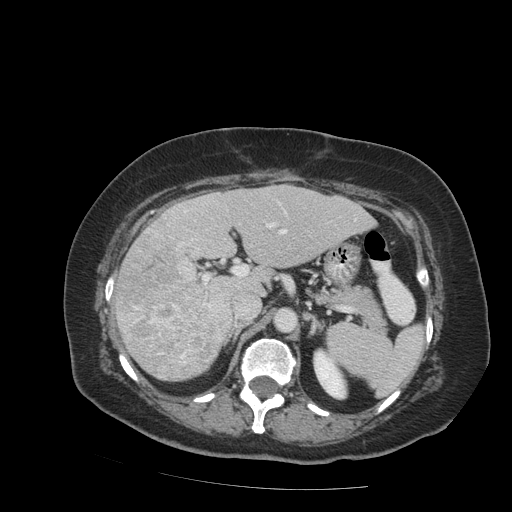
Contrast-enhanced abdominal CT (liver protocol), one axial slice. Slice 49 of 99 in the series (ordered by position). 140 kVp. Soft-tissue window (W 400 / L 40 HU). 2.5 mm slice thickness. 512 × 512 image matrix. From the clinical record (not read from this slice): diagnosis: hepatocellular carcinoma (patient treated with transarterial chemoembolisation; whether this scan precedes or follows treatment is not stated here); TNM stage (as recorded): Stage-IVB; Child-Pugh class: A; tumour differentiation: moderately differentiated.
Outlined on this slice (semi-automatic segmentation, software-assisted and operator-edited):
- liver parenchyma outside the tumour (the mass and vessels are separate outlines, so this box may not span the whole liver): box from (x=114, y=184) to (x=376, y=380) px
- mass: (x=115, y=231)–(x=226, y=379)
- liver vessels: (x=182, y=203)–(x=287, y=306)